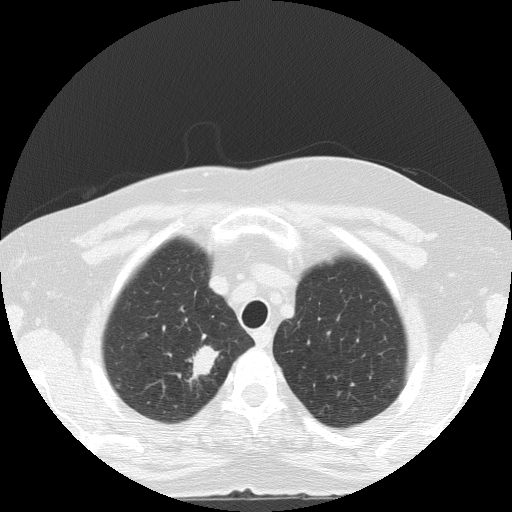
Low-dose screening chest CT, one axial slice; position 113 of 133 along the scan axis; lung window (W 1500 / L -600 HU); 2 mm slice thickness; 512 × 512 image matrix, field of view 320 × 320 mm.
Outlined on this slice (expert manual segmentation):
- lesion 1 (tumor, upper lobe of right lung): bounding box <186,345,219,386> (left, top, right, bottom; pixels)